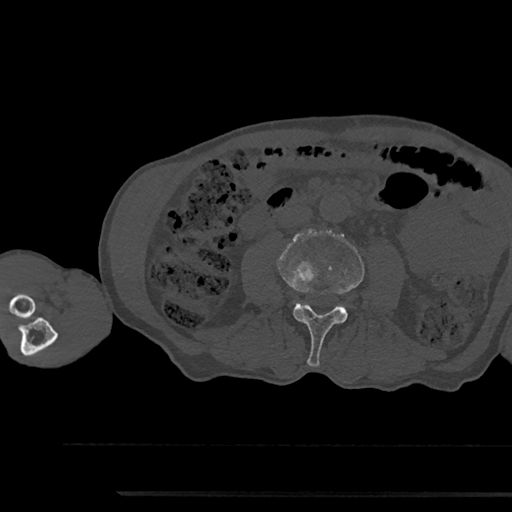
CT including the spine, one axial slice; slice 474 of 797 in the series (ordered by position); 120 kVp; bone window (W 1800 / L 400 HU); 0.5 mm slice thickness; 512 × 512 image matrix, field of view 367 × 367 mm. Male patient, age 79 years. From the clinical record (not read from this slice): primary cancer: prostate.
Outlined on this slice (semi-automatic segmentation, software-assisted and operator-edited):
- L3 vertebra: bounding box (x1, y1, x2, y2) in pixels: (278, 230, 364, 367)